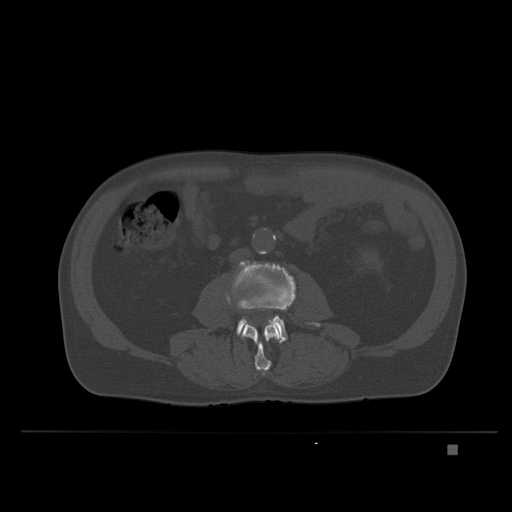
CT including the spine, one axial slice; bone window (W 1800 / L 400 HU); 512 × 512 image matrix. Male patient, age 73 years. From the clinical record (not read from this slice): primary cancer: skin.
Annotated regions visible in this slice (semi-automatically segmented with operator editing):
- L3 vertebra: bounding box (x1, y1, x2, y2) in pixels: (242, 321, 281, 376)
- L4 vertebra: (225, 261, 320, 343)